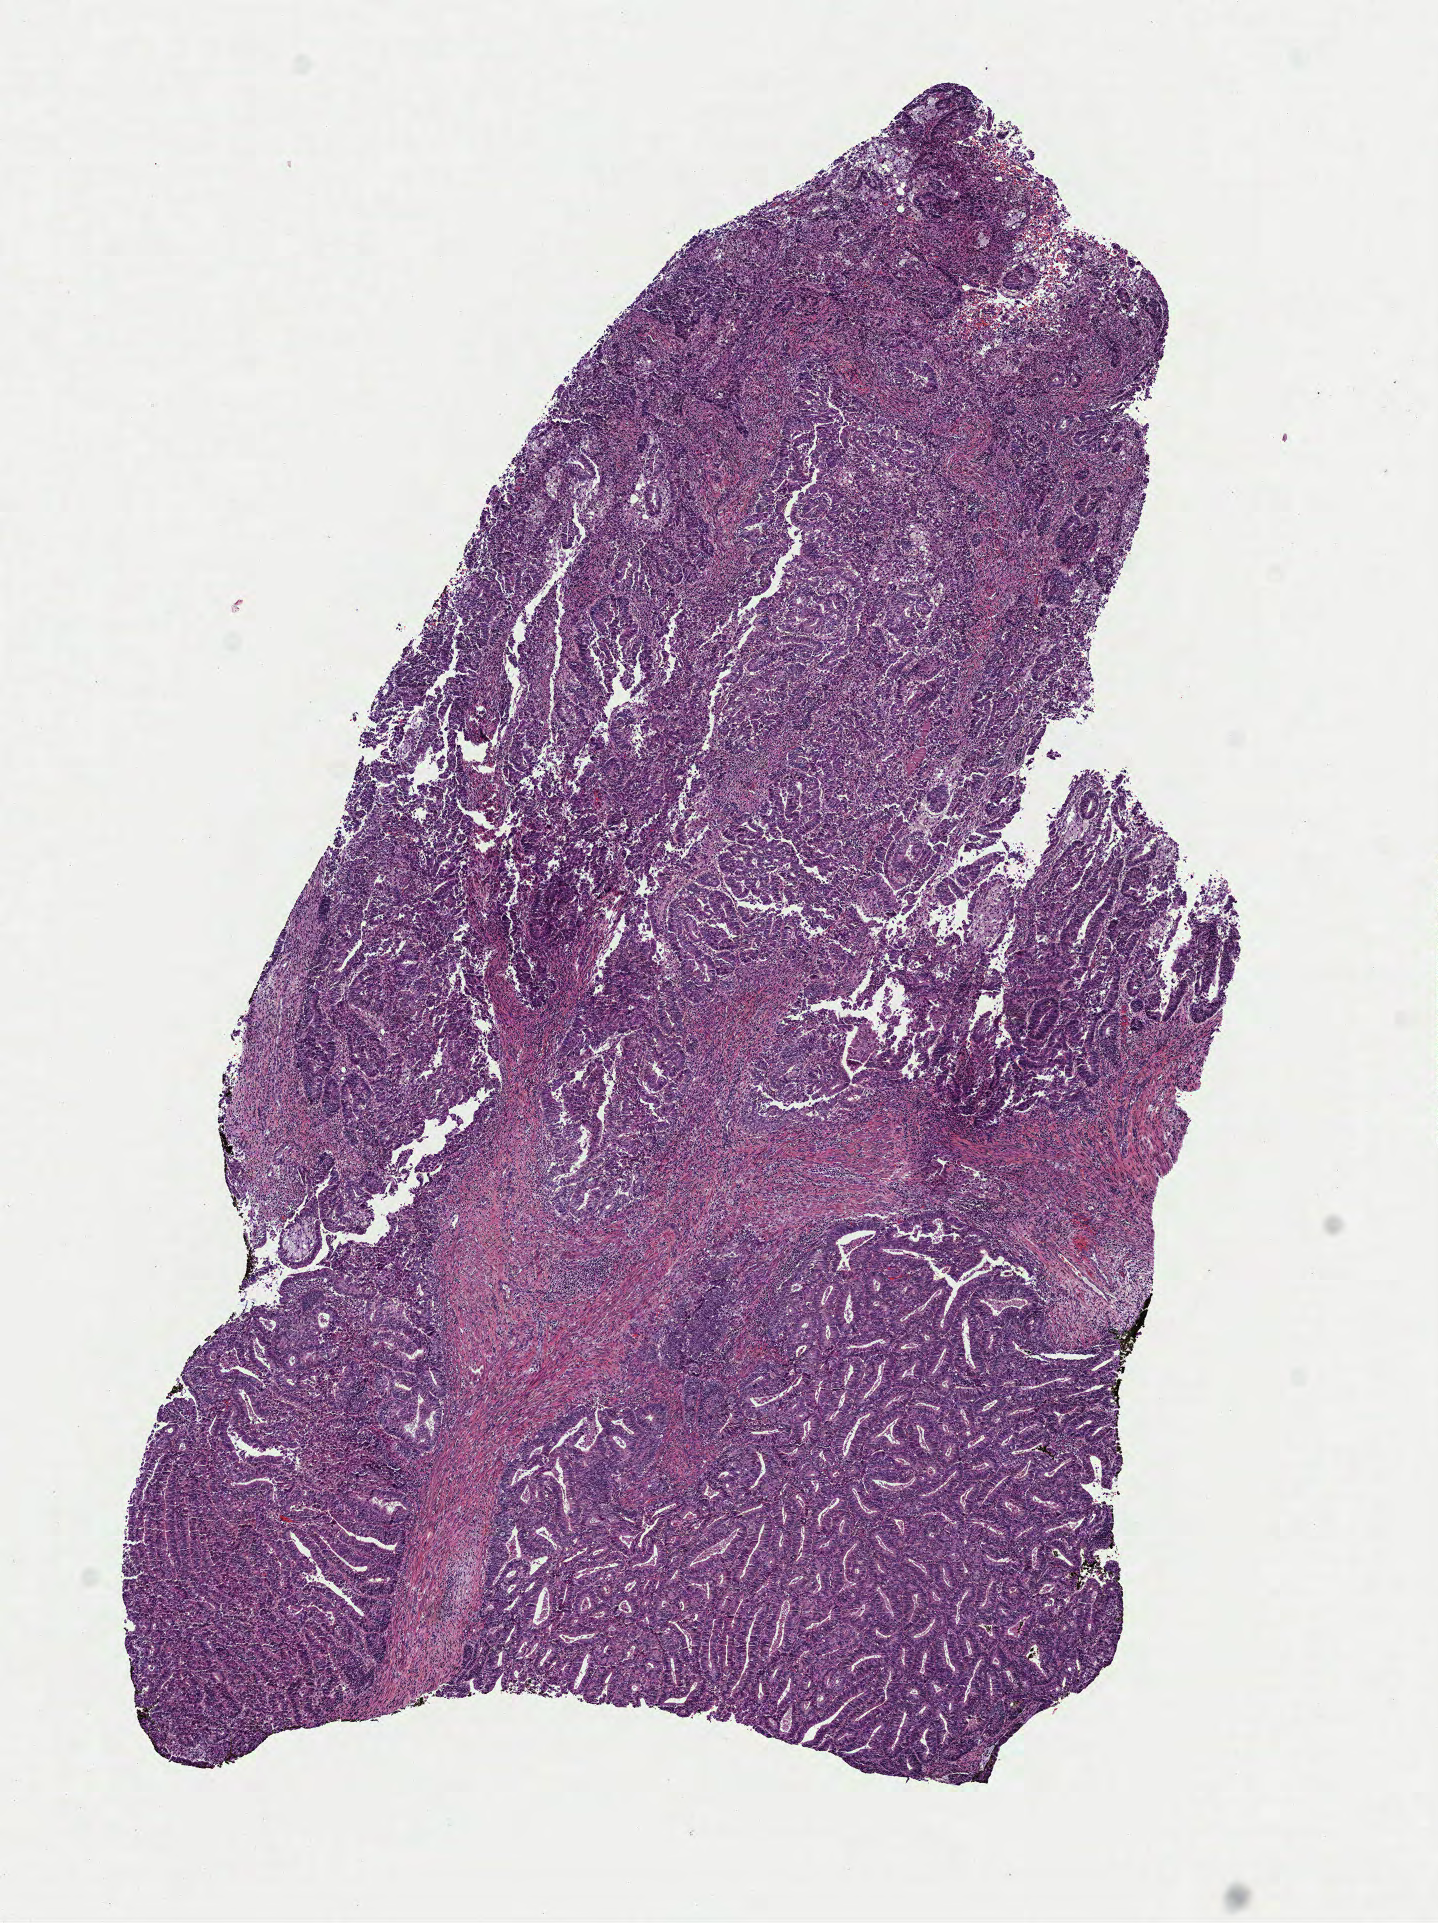
H&E whole-slide image, low-resolution overview of the scanned area, about 5.8 x 7.8 mm; formalin-fixed paraffin-embedded (FFPE) diagnostic section; sample: primary tumour, uterus. Female patient; age at initial diagnosis 58 years. Histologic grade: G2 (moderately differentiated).
* histologic diagnosis: Endometrioid adenocarcinoma, NOS (endometrium)
* FIGO stage: IB